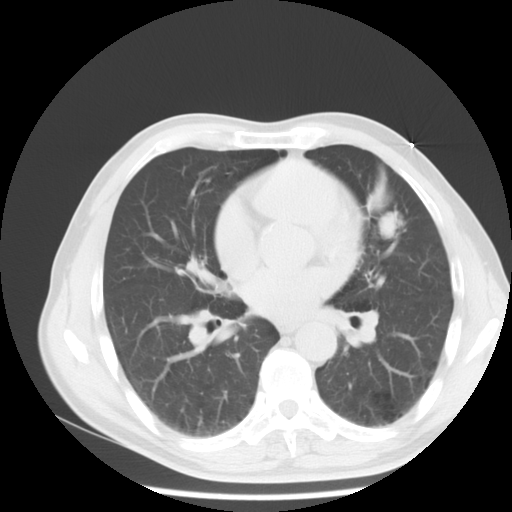
Chest CT, one axial slice. Slice 5 of 13 in the series (ordered by position). Reconstruction kernel STANDARD. 120 kVp. Lung window (W 1500 / L -600 HU). 5 mm slice thickness. 512 × 512 image matrix, field of view 350 × 350 mm. Male patient, age 54 years. From the clinical record (not read from this slice): clinical TNM (as recorded): T1c N0 M0.
Outlined on this slice (bounding box drawn by a radiologist):
- lung tumour (recorded histology: adenocarcinoma): bounding box [x1, y1, x2, y2] px = [366, 192, 405, 246]